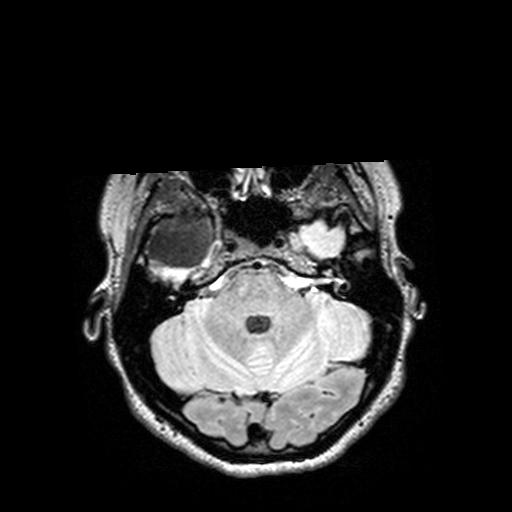
Brain MRI from a brain-tumour surgery series, one axial slice. Slice 107 of 144 in the series (ordered by position). T2 FLAIR. 1 mm slice thickness. 512 × 512 image matrix, field of view 250 × 250 mm. Case-level facts recorded for this patient, not image findings: histopathology: Astrocytoma; WHO grade: 3; IDH mutation: yes.
Annotated regions visible in this slice (manually delineated by an expert):
- tumour: bounding box [x1, y1, x2, y2] px = [126, 213, 232, 273]